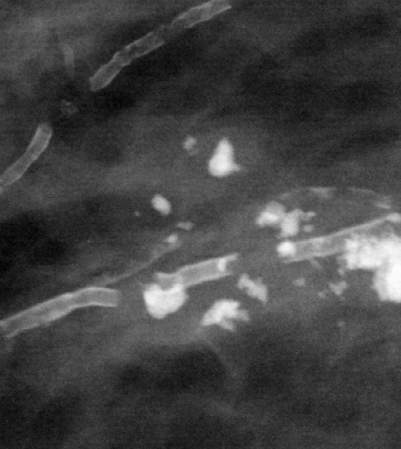
Region of interest cut from a scanned film mammogram (one marked finding); right breast; MLO view; BI-RADS breast density category 1 (scale 1–4).
Marked abnormality: calcifications, morphology coarse / pleomorphic, distribution clustered; BI-RADS assessment category 2; subtlety rating 5 on a 1 (subtle) to 5 (obvious) scale; pathology result (as recorded, not read from the image): benign.